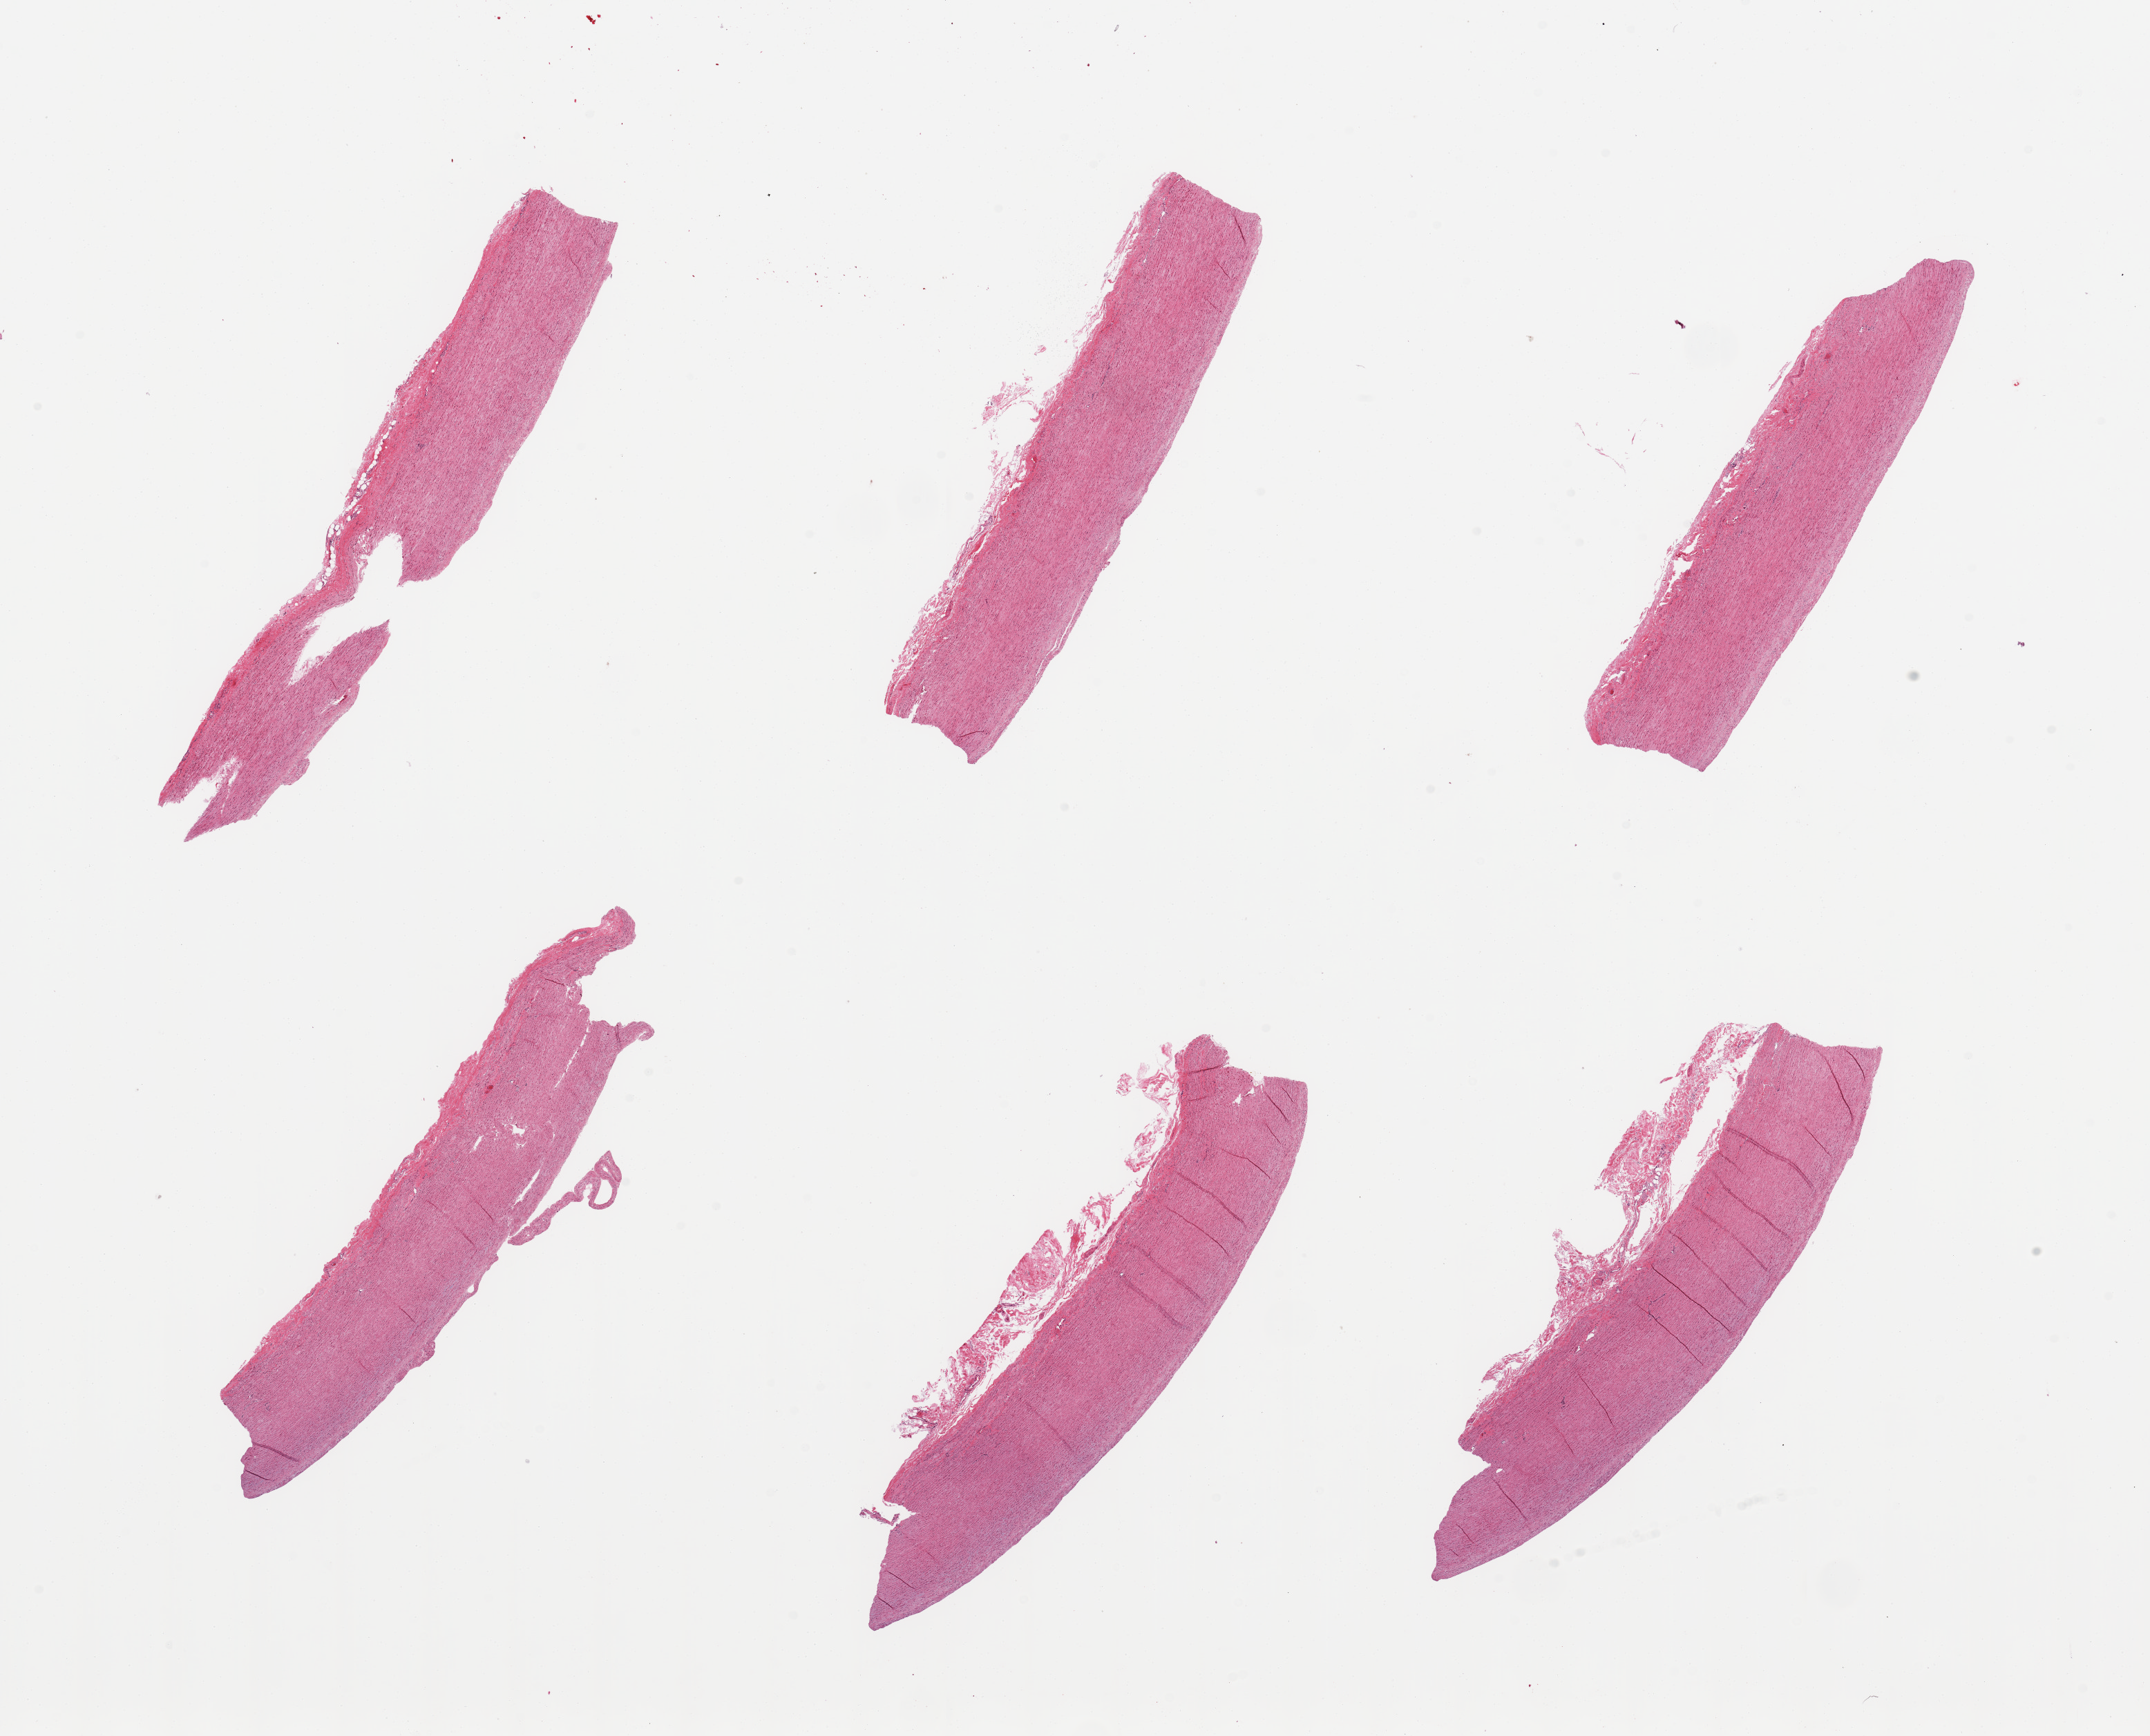
Whole-slide image, hematoxylin and eosin (H&E) stain, a low-resolution overview of the entire scanned area, about 24.6 x 19.9 mm, PAXgene-fixed, paraffin-embedded tissue, section of aorta (target tissue), tissue donor sample. Donor sex: male.
• pathologist's review note for this sample: 6 pieces, minimal atherosis